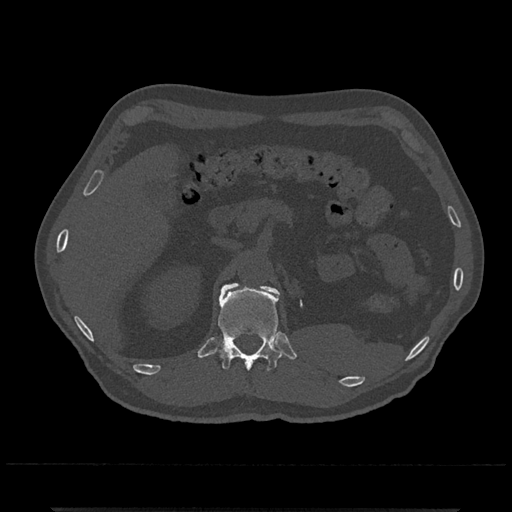
CT including the spine, one axial slice; 120 kVp; bone window (W 1800 / L 400 HU); 0.5 mm slice thickness; 512 × 512 image matrix. Patient: male, 67 years. Case-level facts recorded for this patient, not image findings: primary cancer: prostate.
Annotated regions visible in this slice (semi-automatically segmented with operator editing):
- L1 vertebra: bounding box (x1, y1, x2, y2) in pixels: (258, 284, 275, 292)
- T12 vertebra: (215, 283, 282, 371)